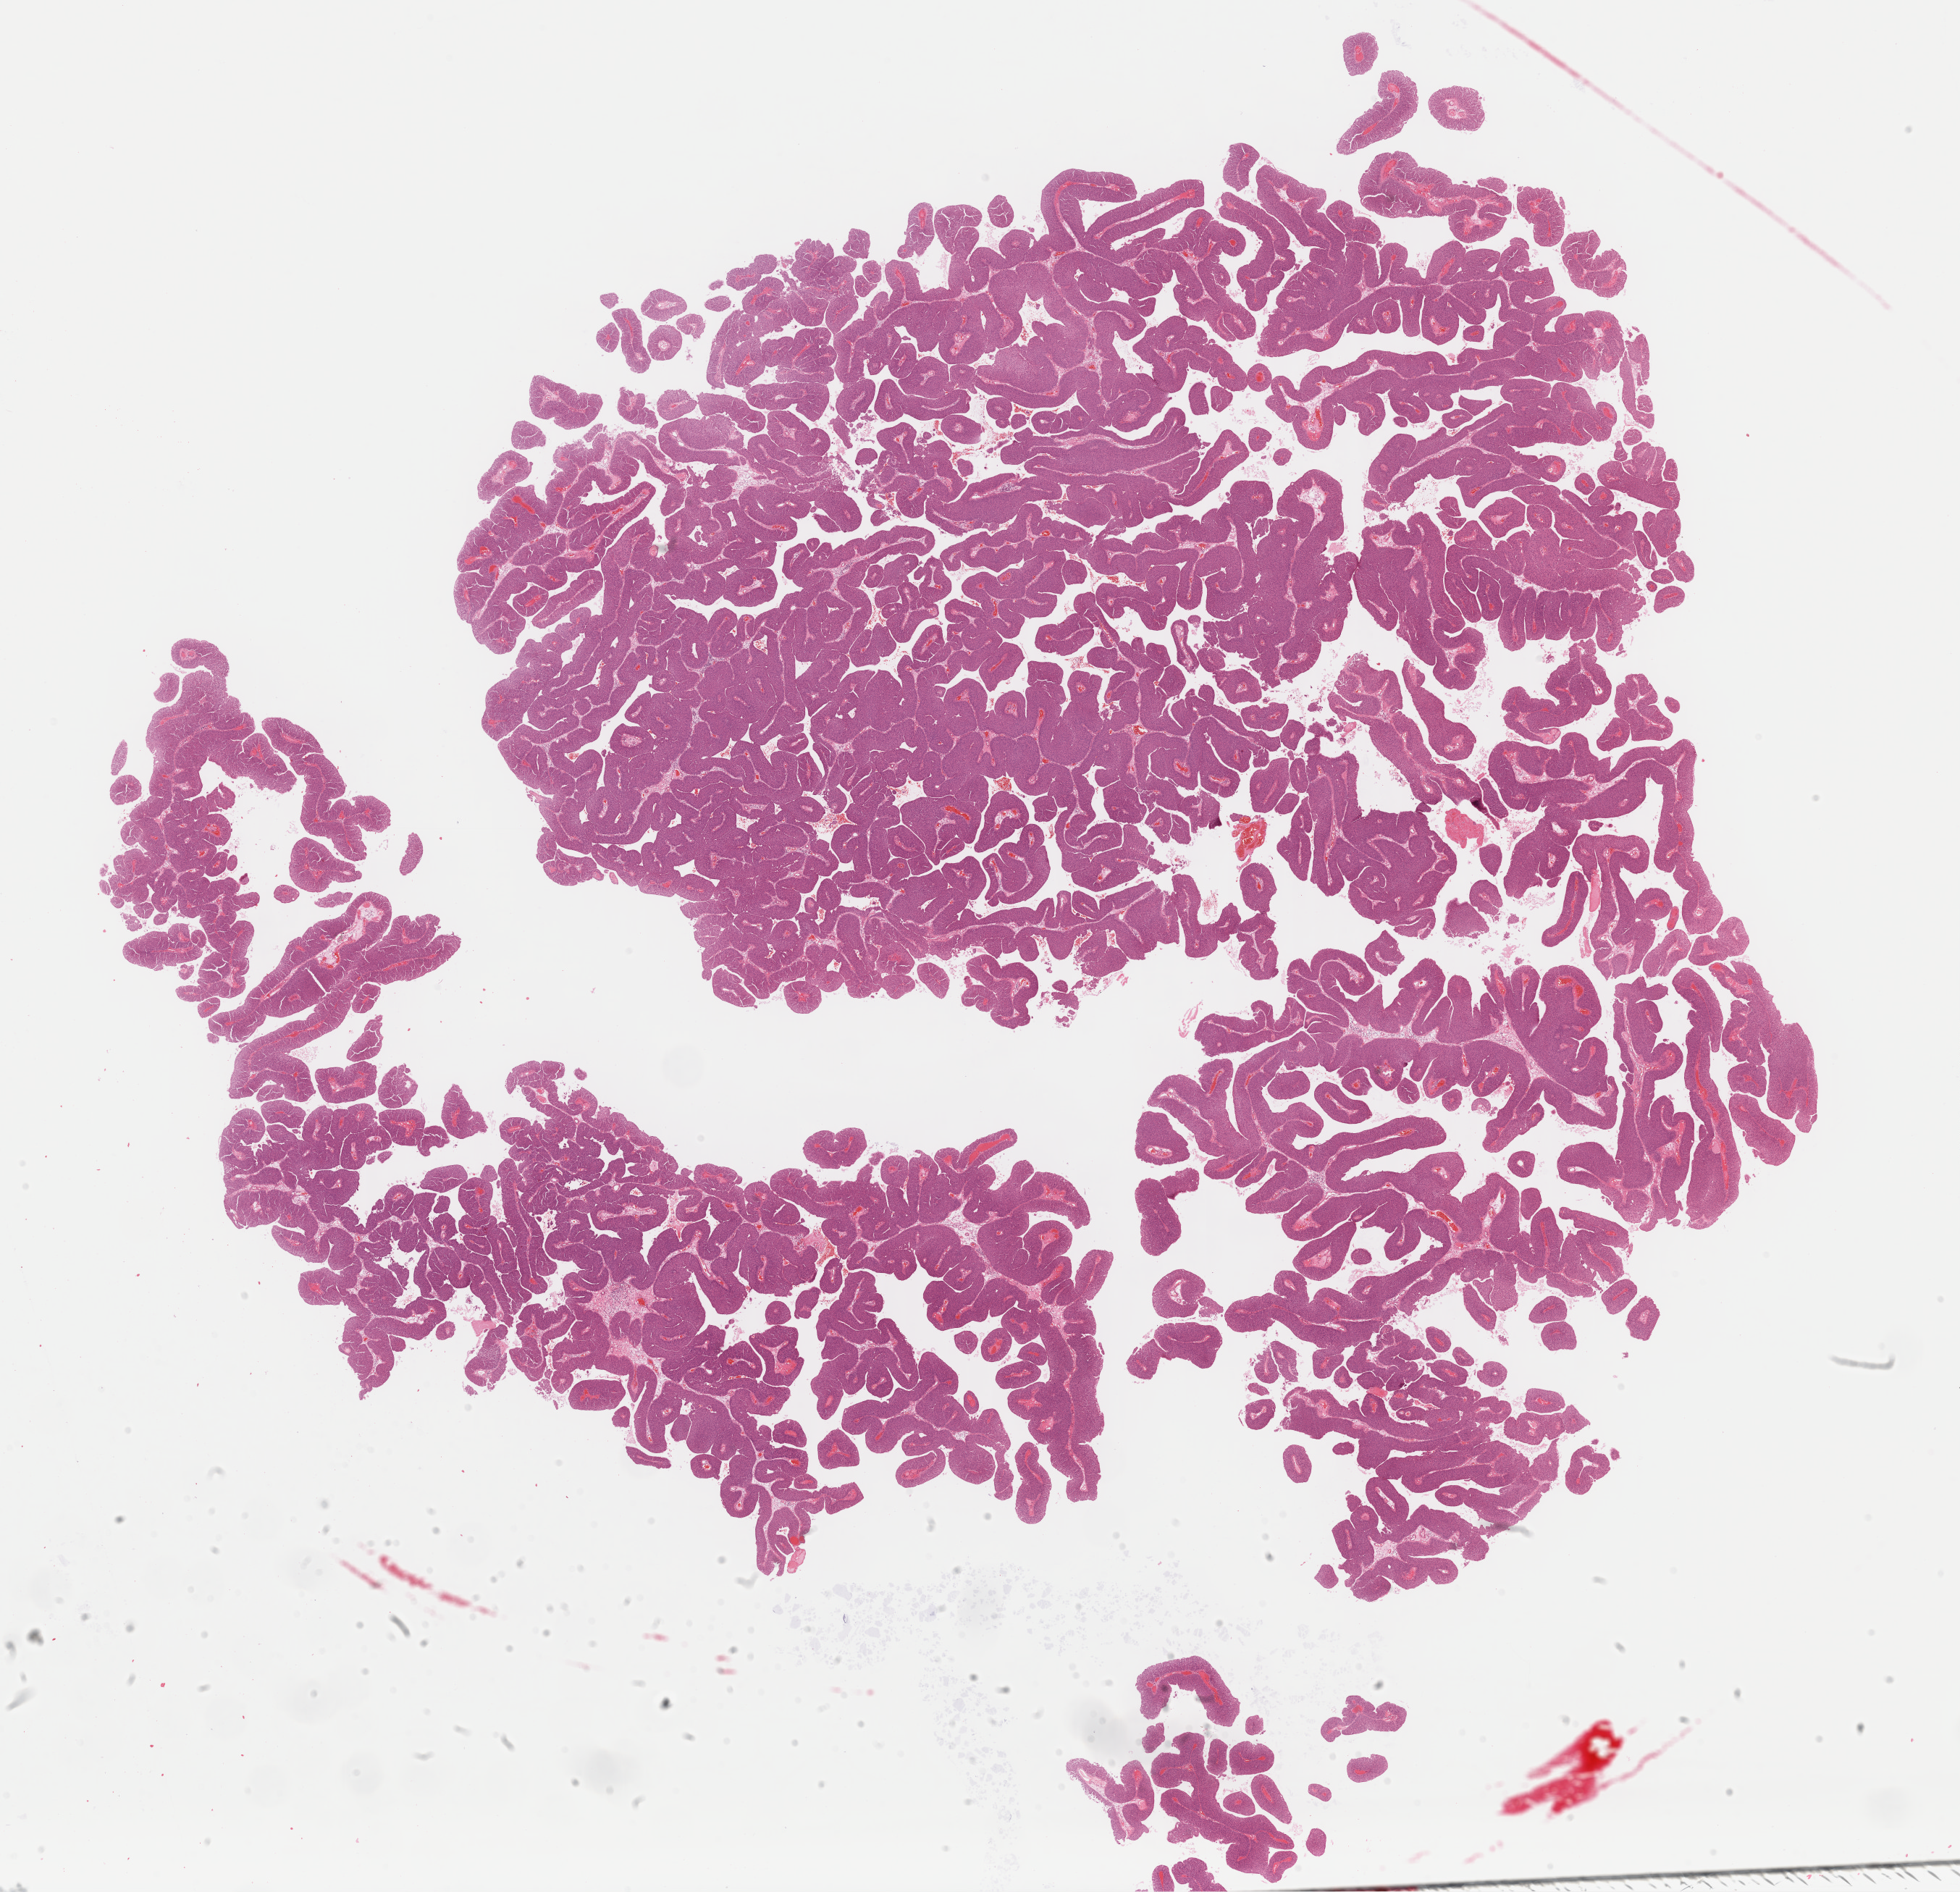
Hematoxylin and eosin (H&E) stained whole-slide image, whole scanned area (about 21.4 x 20.6 mm) shown as a low-resolution overview; formalin-fixed paraffin-embedded (FFPE) diagnostic section; sample: primary tumour, bladder. Male, age 67 years at initial diagnosis. Histologic grade: low grade.
• histologic diagnosis: Transitional cell carcinoma
• AJCC pathologic stage: II (7th edition)